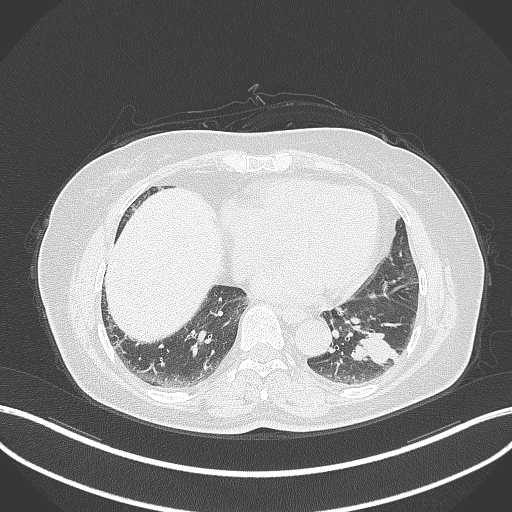
Chest CT, one axial slice; position 130 of 311 along the scan axis; lung window (W 1500 / L -600 HU); 1 mm slice thickness; 512 × 512 image matrix, field of view 400 × 400 mm. Female patient, age 59 years. From the clinical record (not read from this slice): clinical TNM (as recorded): T2a N0 M0; histopathological grade: G2-3.
Structures marked on this image (rectangle marked by the reading radiologist):
- lung tumour (recorded histology: adenocarcinoma): bounding box [x1, y1, x2, y2] px = [348, 327, 397, 372]